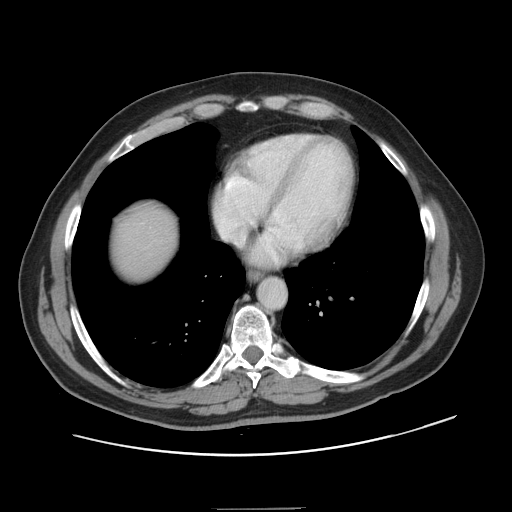
Contrast-enhanced abdominal CT, one axial slice; position 140 of 143 along the scan axis; 120 kVp; intravenous contrast given; soft-tissue window (W 400 / L 40 HU); 2.5 mm slice thickness; 512 × 512 image matrix. Male patient, age 62 years. Case-level facts recorded for this patient, not image findings: diagnosis: colorectal cancer liver metastases, imaged before liver resection; multiple liver metastases: yes; largest metastasis: 2.7 cm; disease in both lobes: no.
Structures marked on this image (expert manual segmentation):
- liver: bounding box (x1, y1, x2, y2) in pixels: (113, 209, 177, 279)
- planned liver remnant (the part of the liver to remain after resection): (112, 210, 177, 280)